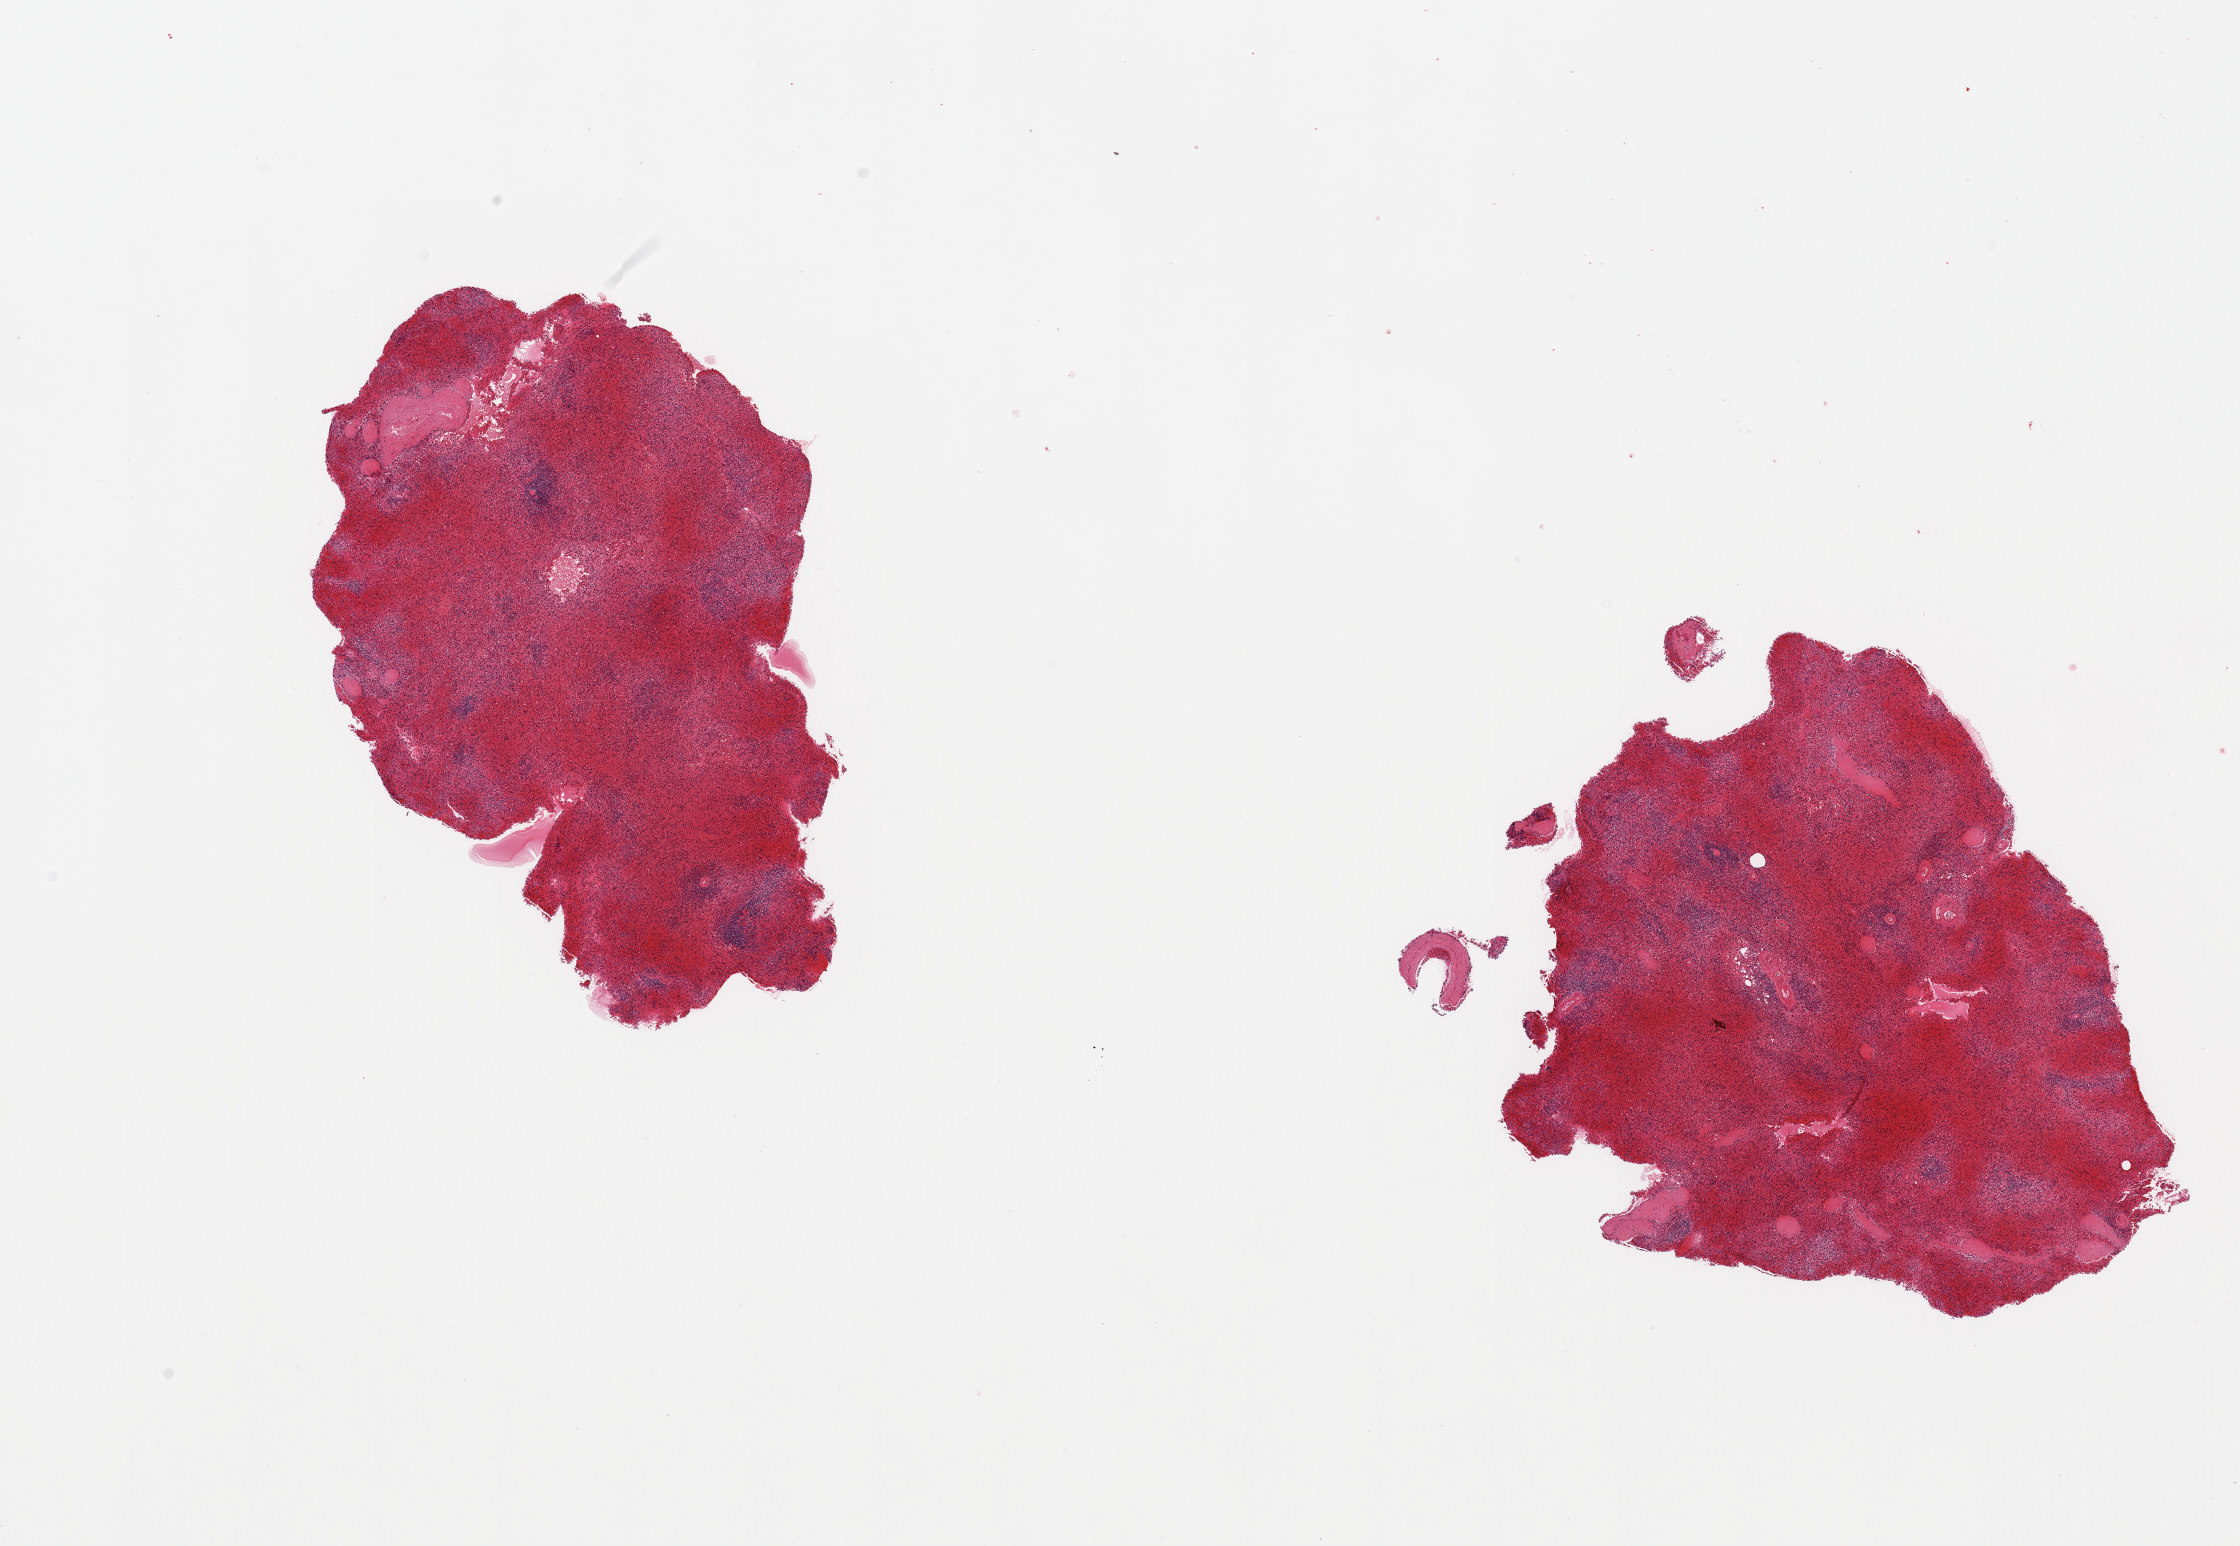
Haematoxylin and eosin whole-slide image, brightfield — low-resolution overview of the scanned area, about 17.7 x 12.2 mm (acquisition: 20x scan), PAXgene-fixed paraffin-embedded (PFPE) section, section of spleen (target tissue), tissue donor sample. Female donor.
Review note (as recorded): 2 pieces; severe congestion.